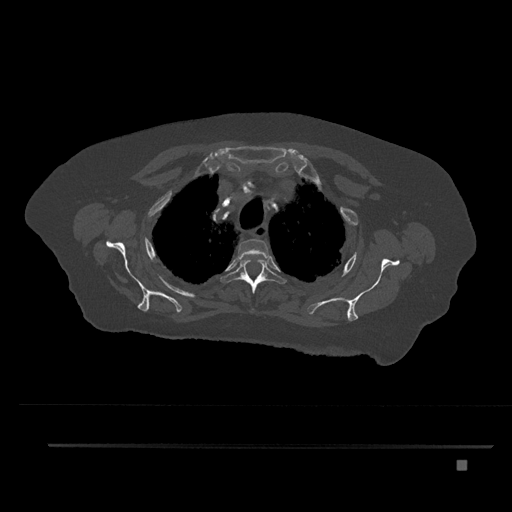
CT including the spine, one axial slice. Slice 645 of 797 in the series (ordered by position). 120 kVp. Bone window (W 1800 / L 400 HU). 0.5 mm slice thickness. 512 × 512 image matrix, field of view 437 × 437 mm. Patient: female, 76 years. Case-level facts recorded for this patient, not image findings: primary cancer: lung; vertebrae with lytic lesions (as recorded): T11, L3.
Outlined on this slice (semi-automatically segmented with operator editing):
- T2 vertebra: bounding box [x1, y1, x2, y2] px = [237, 239, 270, 261]
- T3 vertebra: [221, 256, 286, 294]